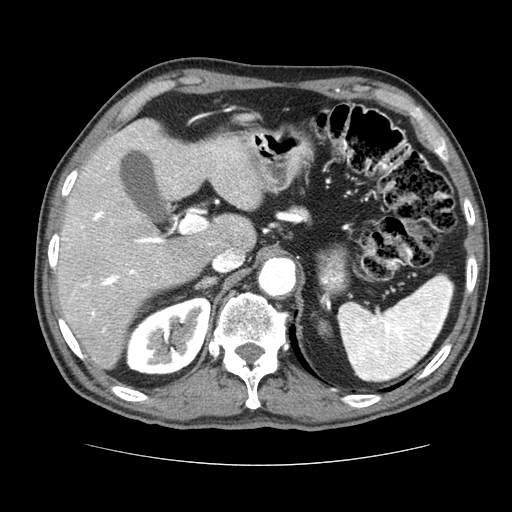
Contrast-enhanced abdominal CT (liver protocol), one axial slice. Position 46 of 79 along the scan axis. Soft-tissue window (W 400 / L 40 HU). 2.5 mm slice thickness. 512 × 512 image matrix, field of view 360 × 360 mm. Case-level facts recorded for this patient, not image findings: diagnosis: hepatocellular carcinoma (patient treated with transarterial chemoembolisation; whether this scan precedes or follows treatment is not stated here); TNM stage (as recorded): Stage-I; Child-Pugh class: A.
Annotated regions visible in this slice (semi-automatically segmented with operator editing):
- liver parenchyma outside the tumour (the mass and vessels are separate outlines, so this box may not span the whole liver): bounding box (x1, y1, x2, y2) in pixels: (56, 118, 262, 368)
- liver vessels: (62, 128, 238, 333)